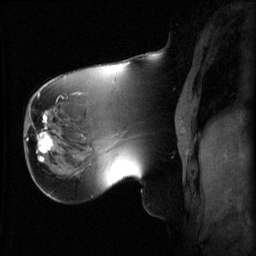
Breast MRI (dynamic contrast-enhanced), one sagittal slice. Slice 20 of 60 in the series (ordered by position). 3 images stored at this slice position (order not interpretable as contrast timing). 1.5 T. TE 4.2 ms, TR 8.2 ms. 2.2 mm slice thickness. 256 × 256 image matrix, field of view 220 × 220 mm. Female patient, age 62 years.
Structures marked on this image (semi-automatically segmented with operator editing):
- analysis volume of interest (the breast-tissue region the enhancement analysis was run in; not a lesion): bounding box [x1, y1, x2, y2] px = [26, 126, 59, 165]
- tumour enhancement mask (voxels above the 70 % enhancement threshold inside the analysis volume of interest): [26, 126, 53, 163]